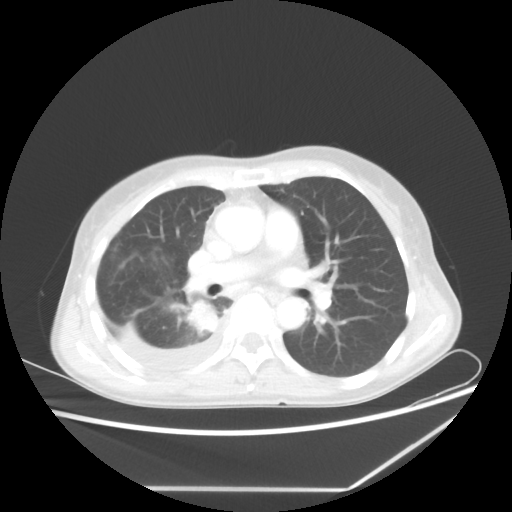
Chest CT, one axial slice; lung window (W 1500 / L -600 HU); 512 × 512 image matrix, field of view 364 × 364 mm. Female patient, age 59 years. Case-level facts recorded for this patient, not image findings: clinical TNM (as recorded): T1c N1 M1.
Outlined on this slice (rectangle marked by the reading radiologist):
- lung tumour (recorded histology: adenocarcinoma): bounding box (x1, y1, x2, y2) in pixels: (185, 298, 220, 334)